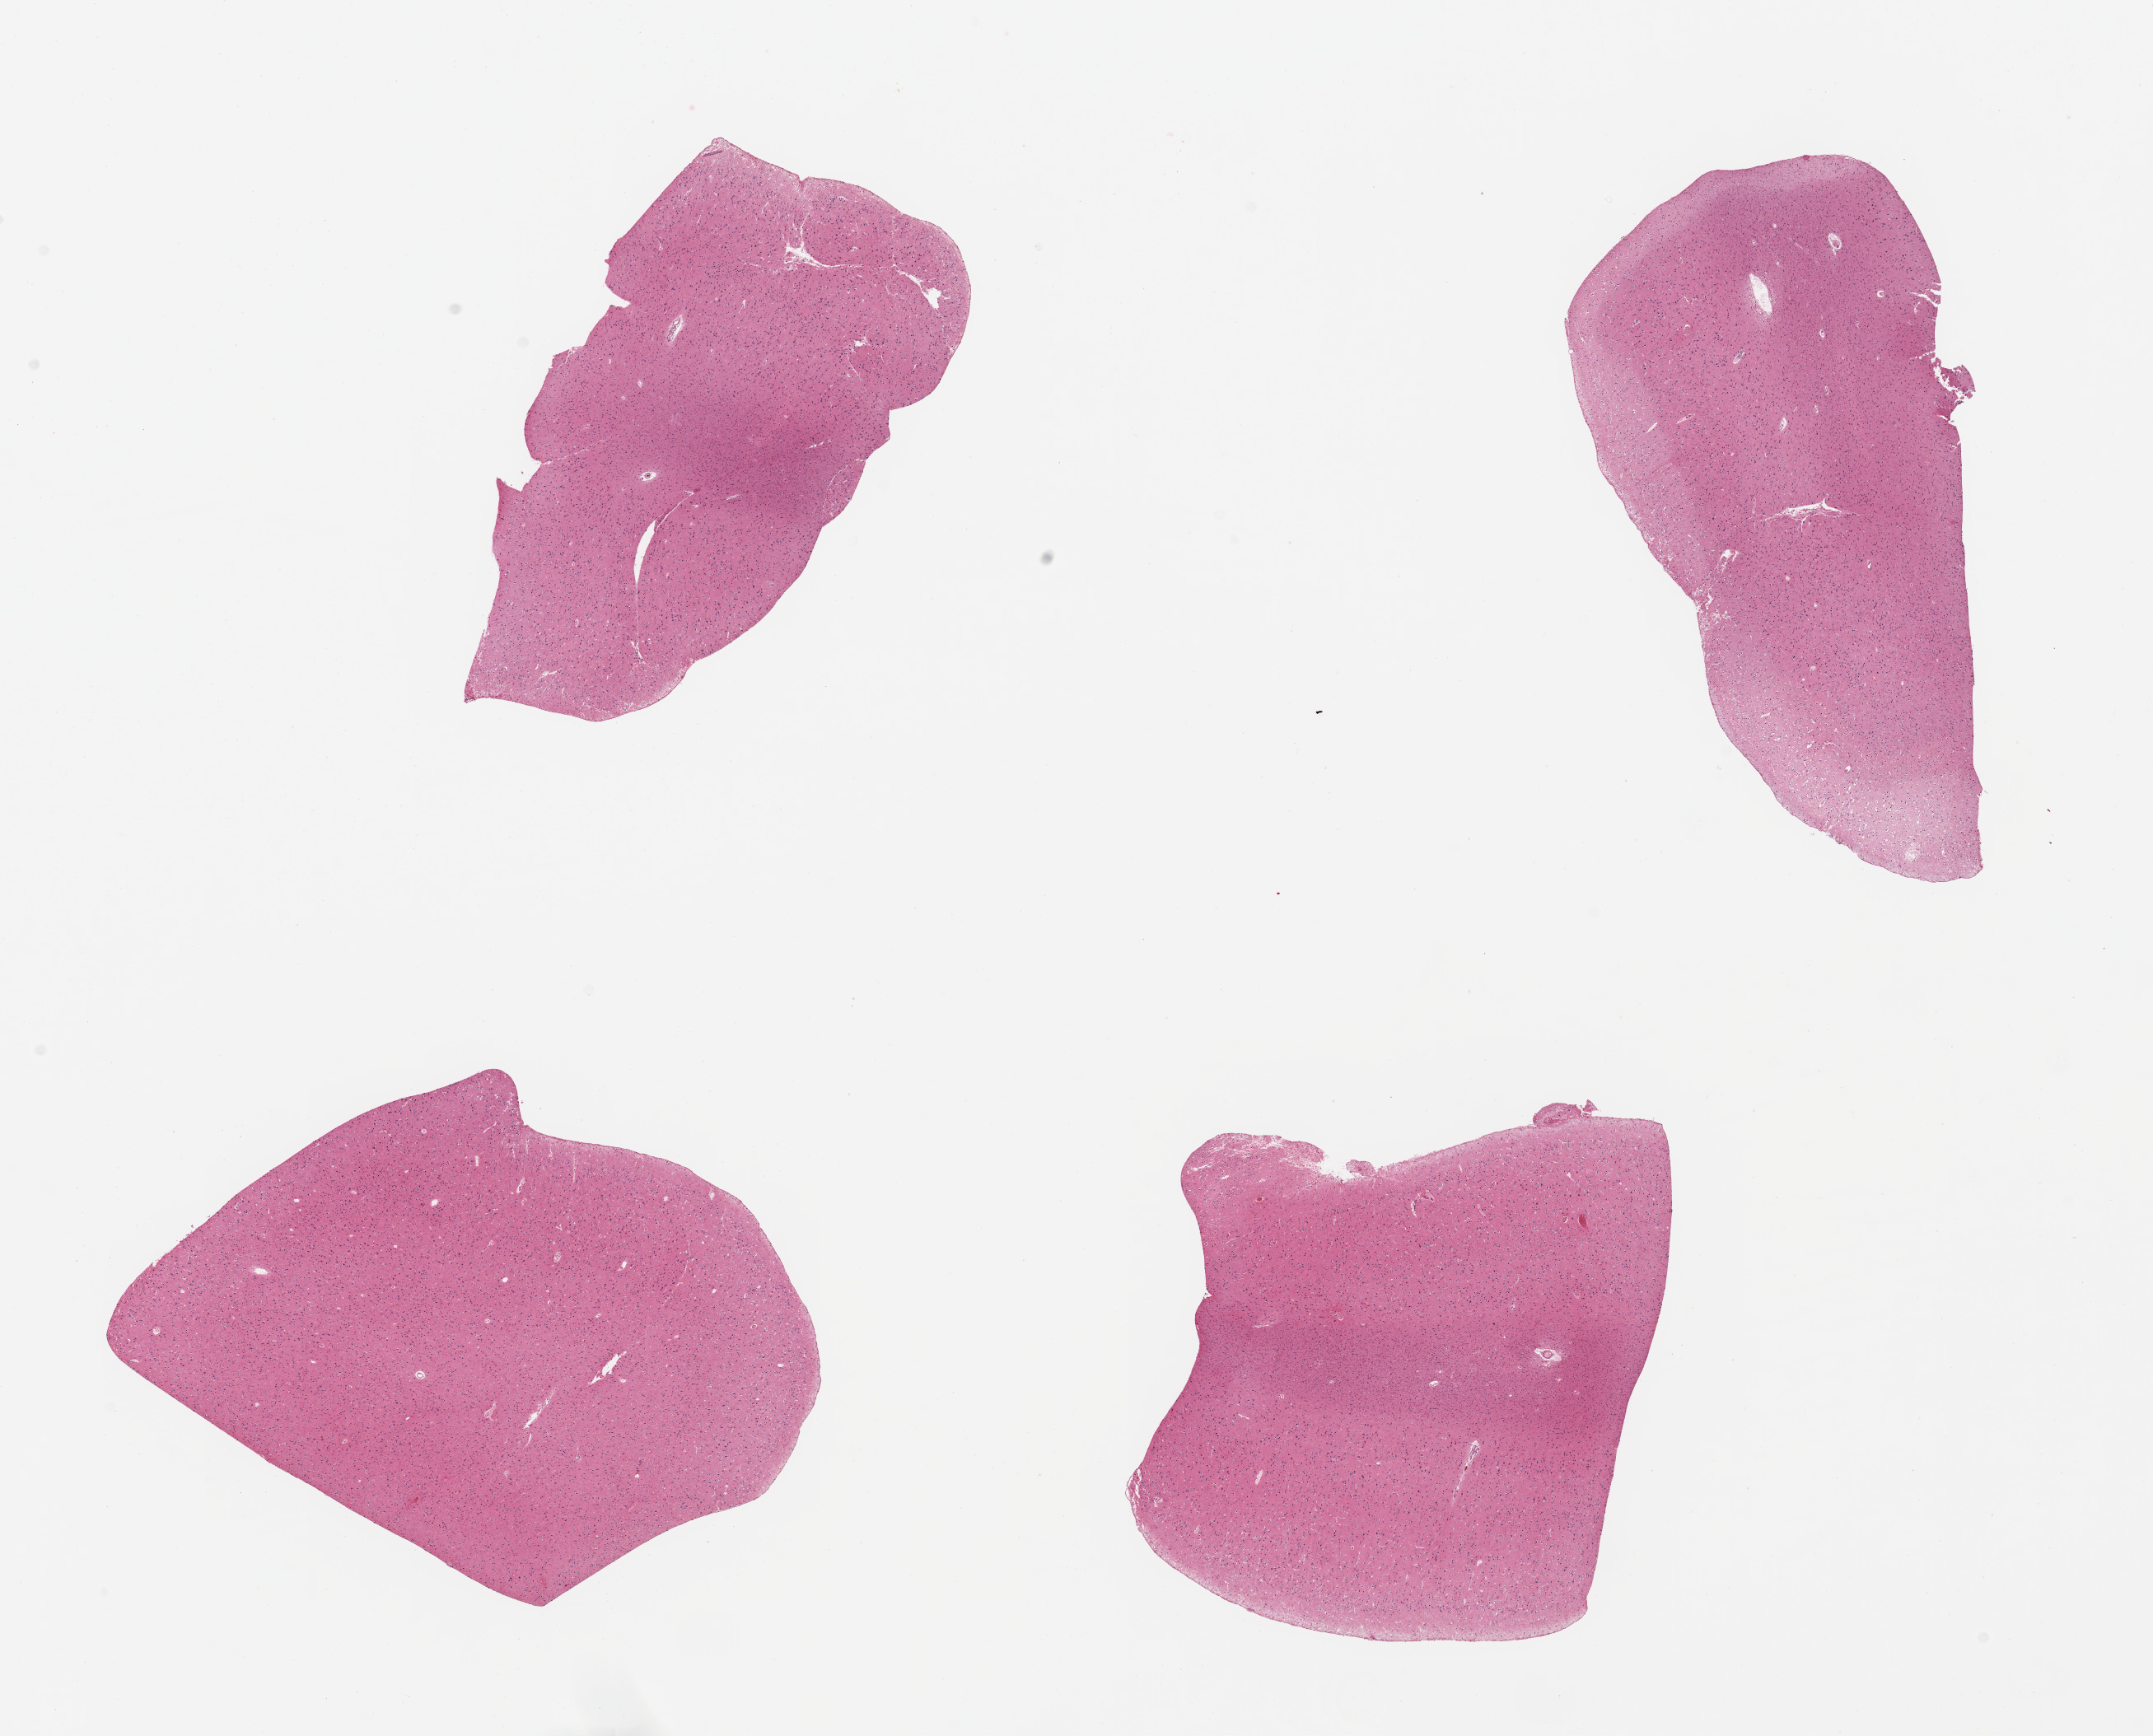
Haematoxylin and eosin whole-slide image, brightfield, shown as a low-resolution overview of the whole scanned area (about 20.7 x 16.7 mm, acquisition: 20x scan). PAXgene-fixed paraffin-embedded (PFPE) section. Target tissue: cerebral cortex. Donor tissue sample. Male donor.
Review note (as recorded): 4 pieces.